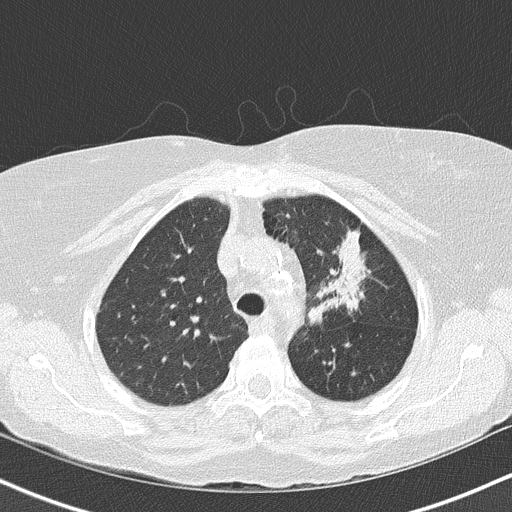
Low-dose screening chest CT, one axial slice; slice 115 of 147 in the series (ordered by position); reconstruction kernel B50f; 120 kVp; lung window (W 1500 / L -600 HU); 2 mm slice thickness; 512 × 512 image matrix, field of view 320 × 320 mm.
Outlined on this slice (expert manual segmentation):
- lesion 1 (tumor, upper lobe of left lung): bounding box (x1, y1, x2, y2) in pixels: (328, 232, 365, 307)